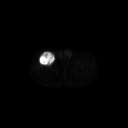
FDG PET of an extremity soft-tissue mass (from a PET/CT study), one axial slice. Position 287 of 311 along the scan axis. 128 × 128 image matrix, field of view 700 × 700 mm. Patient: male, 56 years. From the clinical record (not read from this slice): histological type: pleiomorphic leiomyosarcoma; grade: intermediate; site of the primary tumour: right thigh.
Structures marked on this image (expert contour drawn on MRI and transferred to this co-registered scan by the dataset authors):
- gross tumour volume including surrounding oedema: box from (x=38, y=52) to (x=55, y=66) px
- gross tumour volume (mass): (x=38, y=52)–(x=55, y=66)